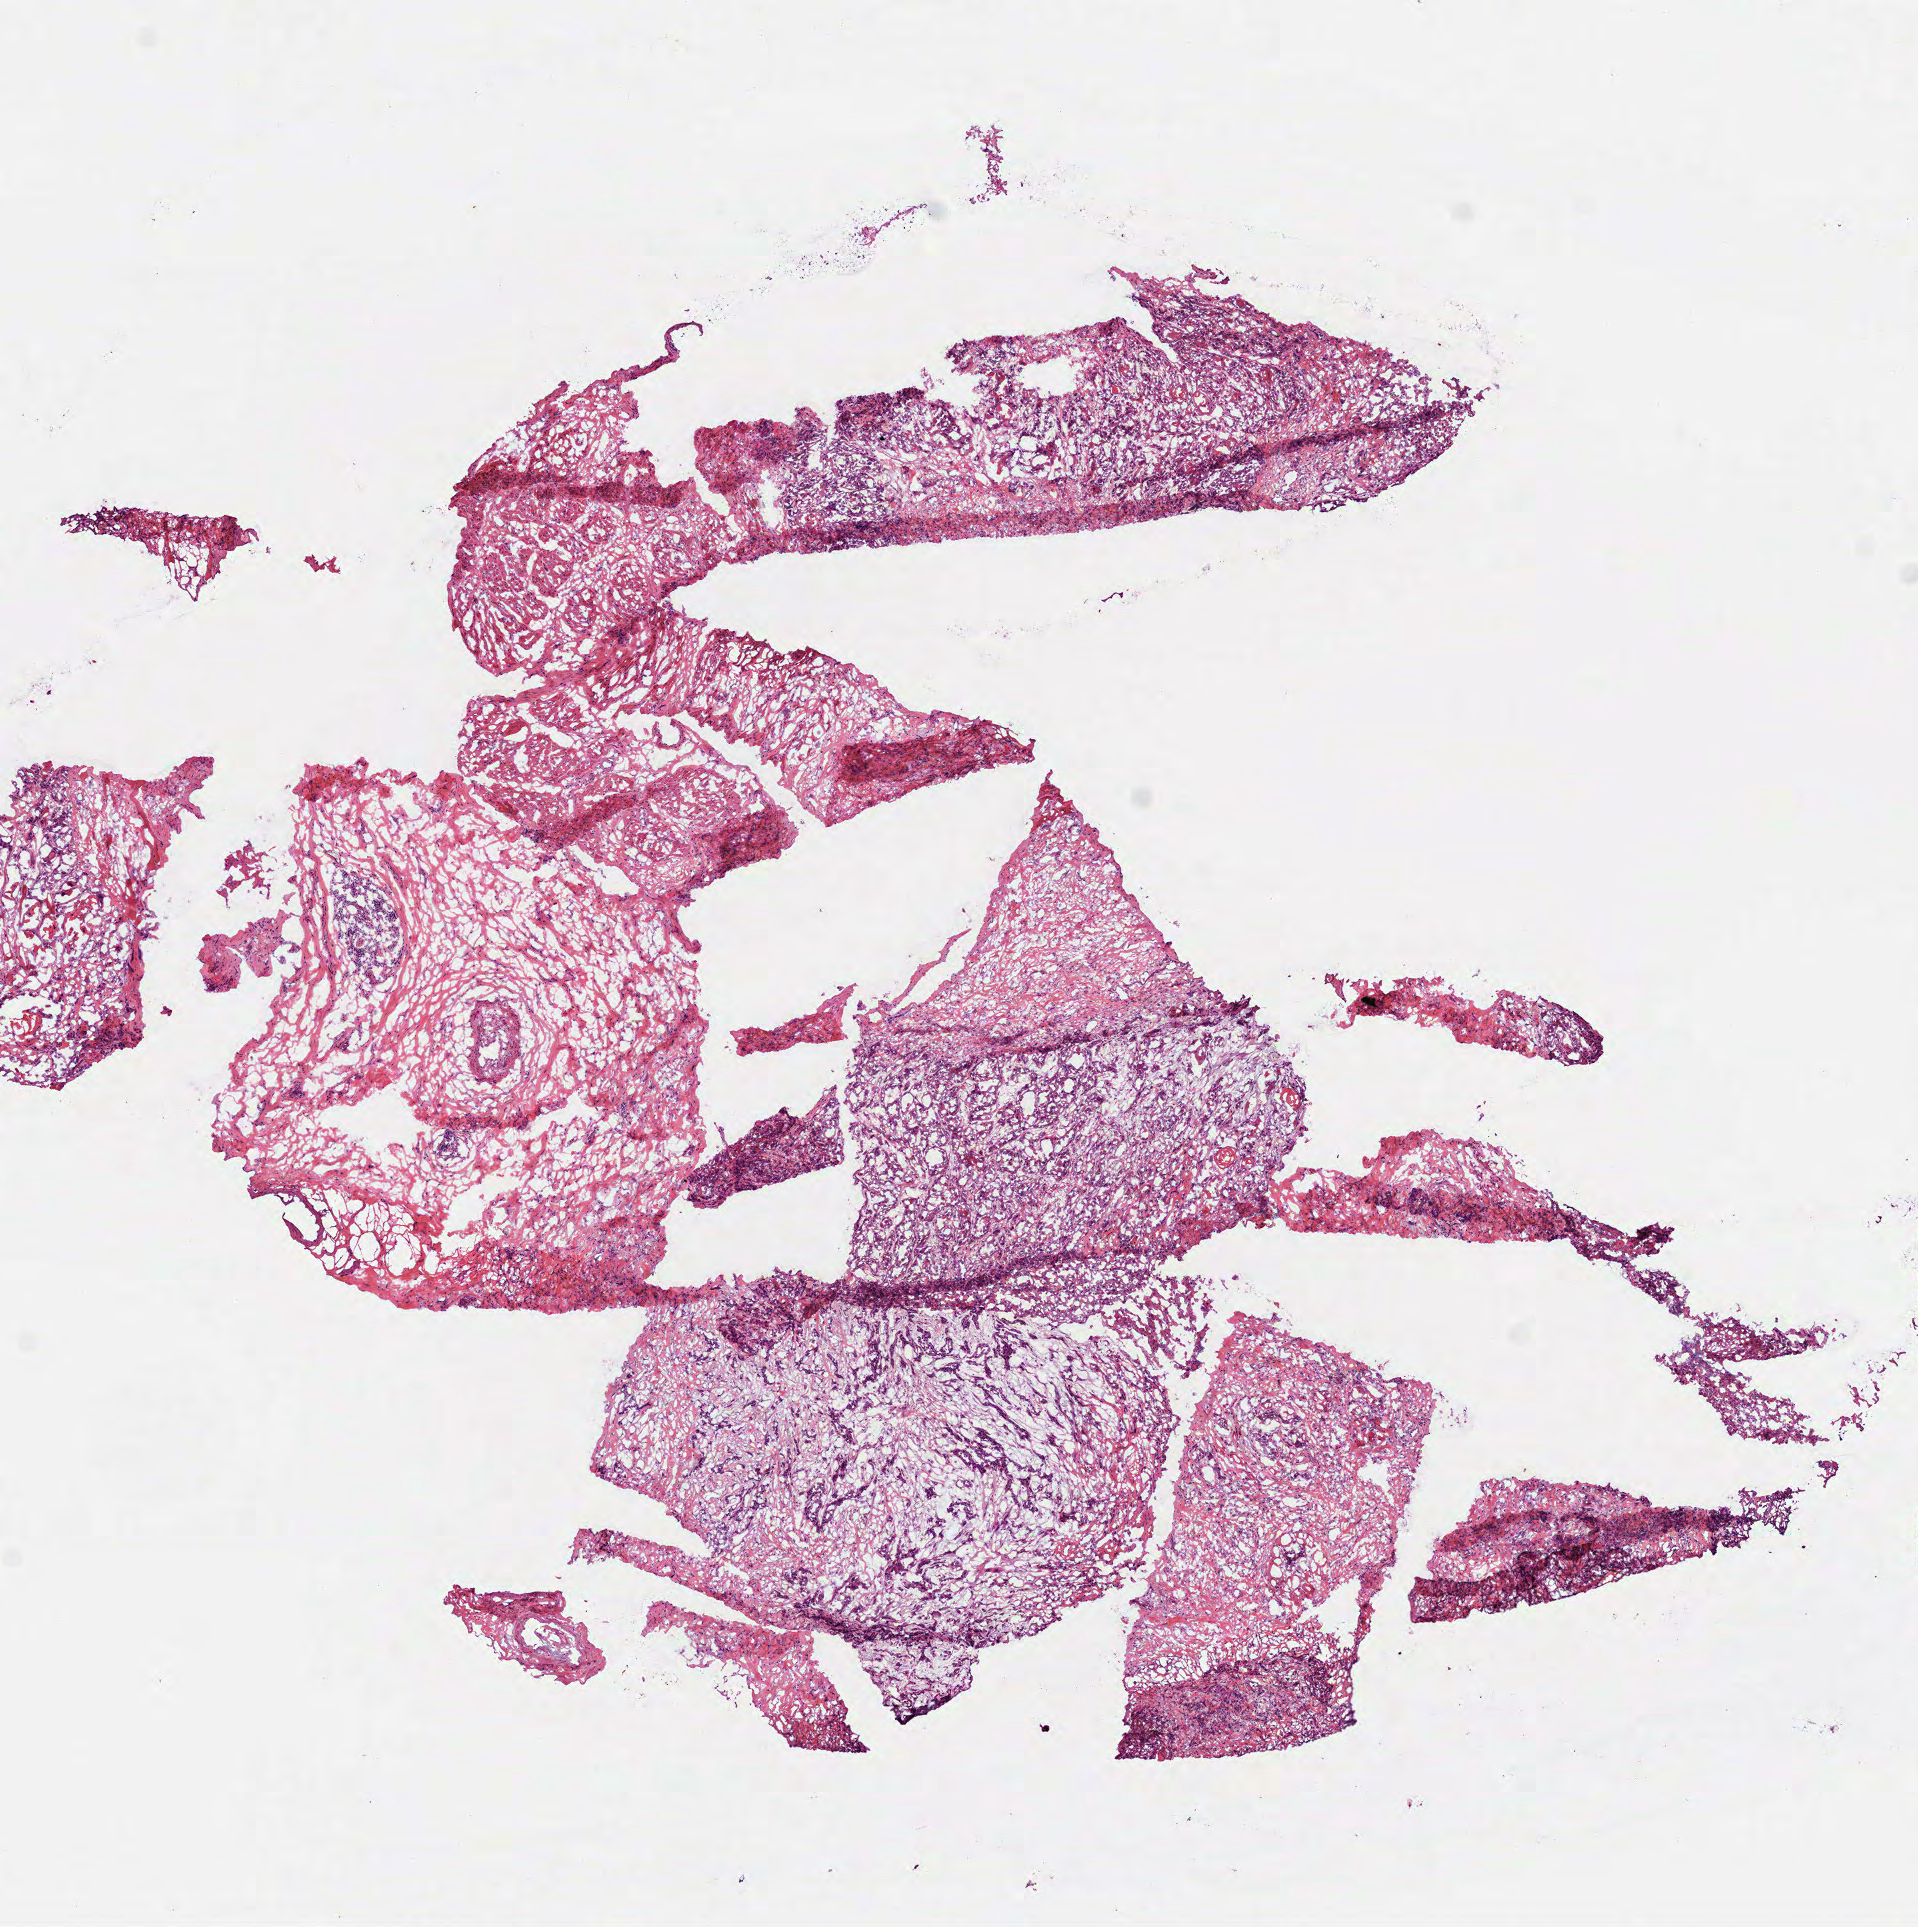
Whole-slide histology image, H&E-stained, whole scanned area (about 7.7 x 7.8 mm, from a 40x scan) shown as a low-resolution overview. Frozen section from the top of the tissue portion. Head and neck, primary tumour sample. Patient: male, age at initial diagnosis 55 years. Histologic grade: G2 (moderately differentiated). Slide review estimates, as recorded: tumour cells 77%, tumour nuclei 75%, normal cells 3%, stromal cells 20%, necrosis 0%.
TNM: T3 N0. Histologic diagnosis: Squamous cell carcinoma, NOS (larynx, NOS). AJCC pathologic stage: III (7th edition).